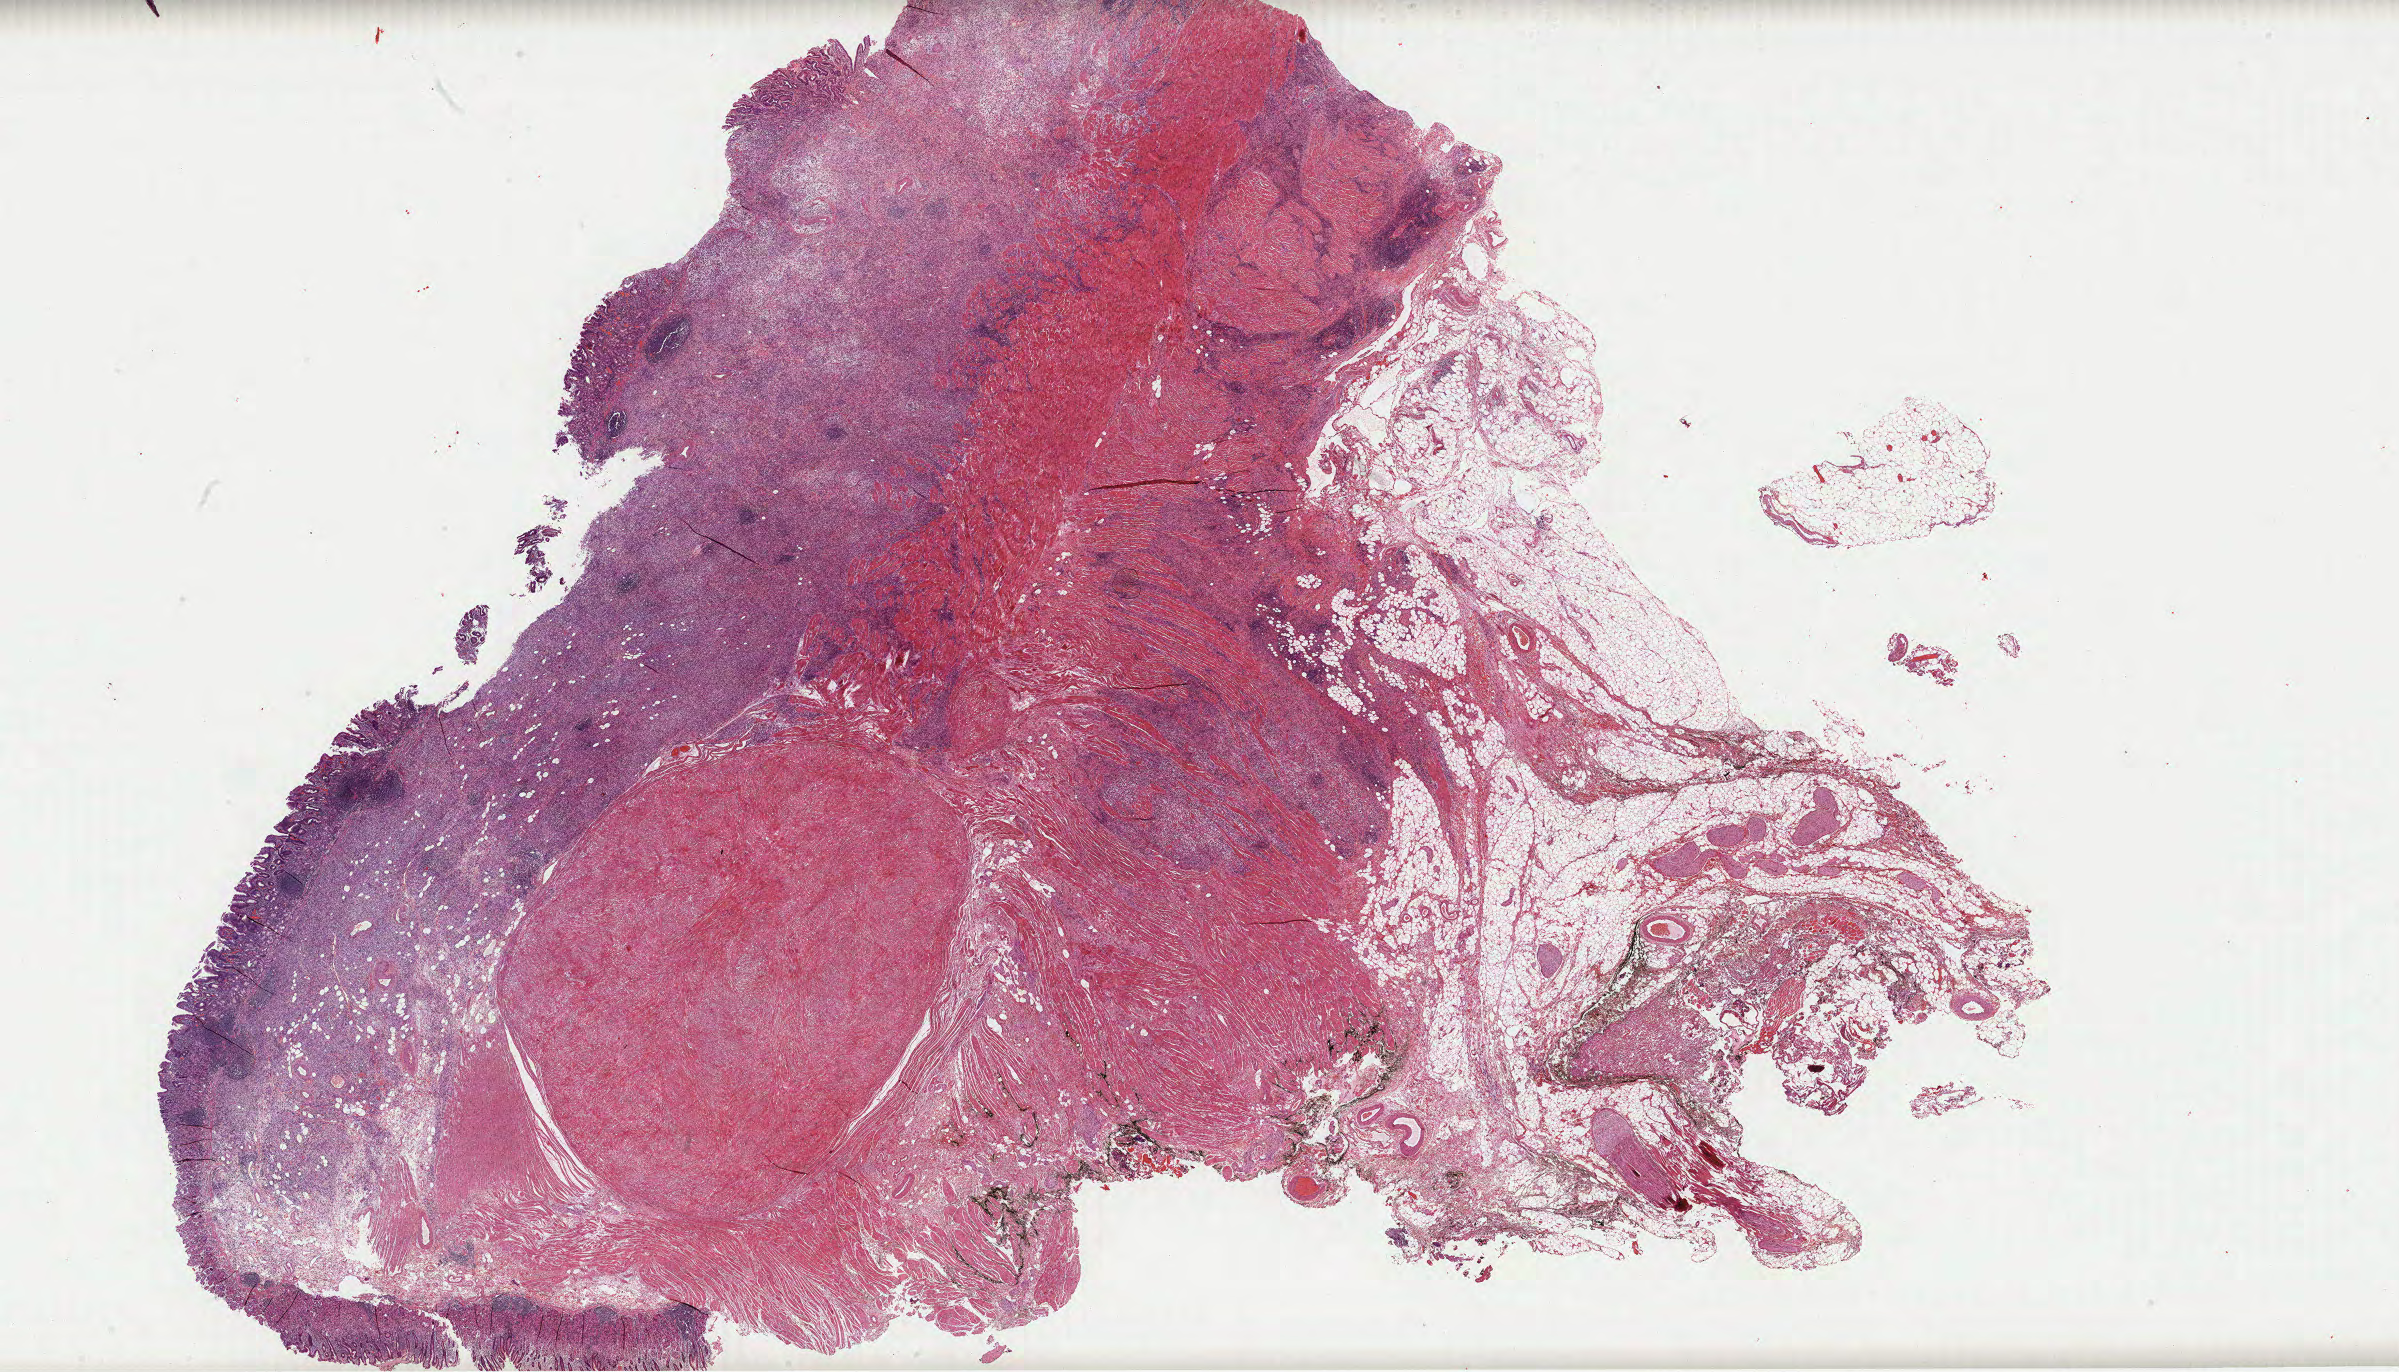
Whole-slide histology image, H&E, whole scanned area (about 38.6 x 22.1 mm, slide scanned at 40x) shown as a low-resolution overview. Formalin-fixed paraffin-embedded (FFPE) diagnostic section. Stomach, primary tumour sample. Female, age 63 years at initial diagnosis. Histologic grade: G3 (poorly differentiated).
AJCC pathologic stage: II. Lymph nodes positive (case pathology): 2 of 4 examined. Histologic diagnosis: Carcinoma, diffuse type (cardia, NOS).